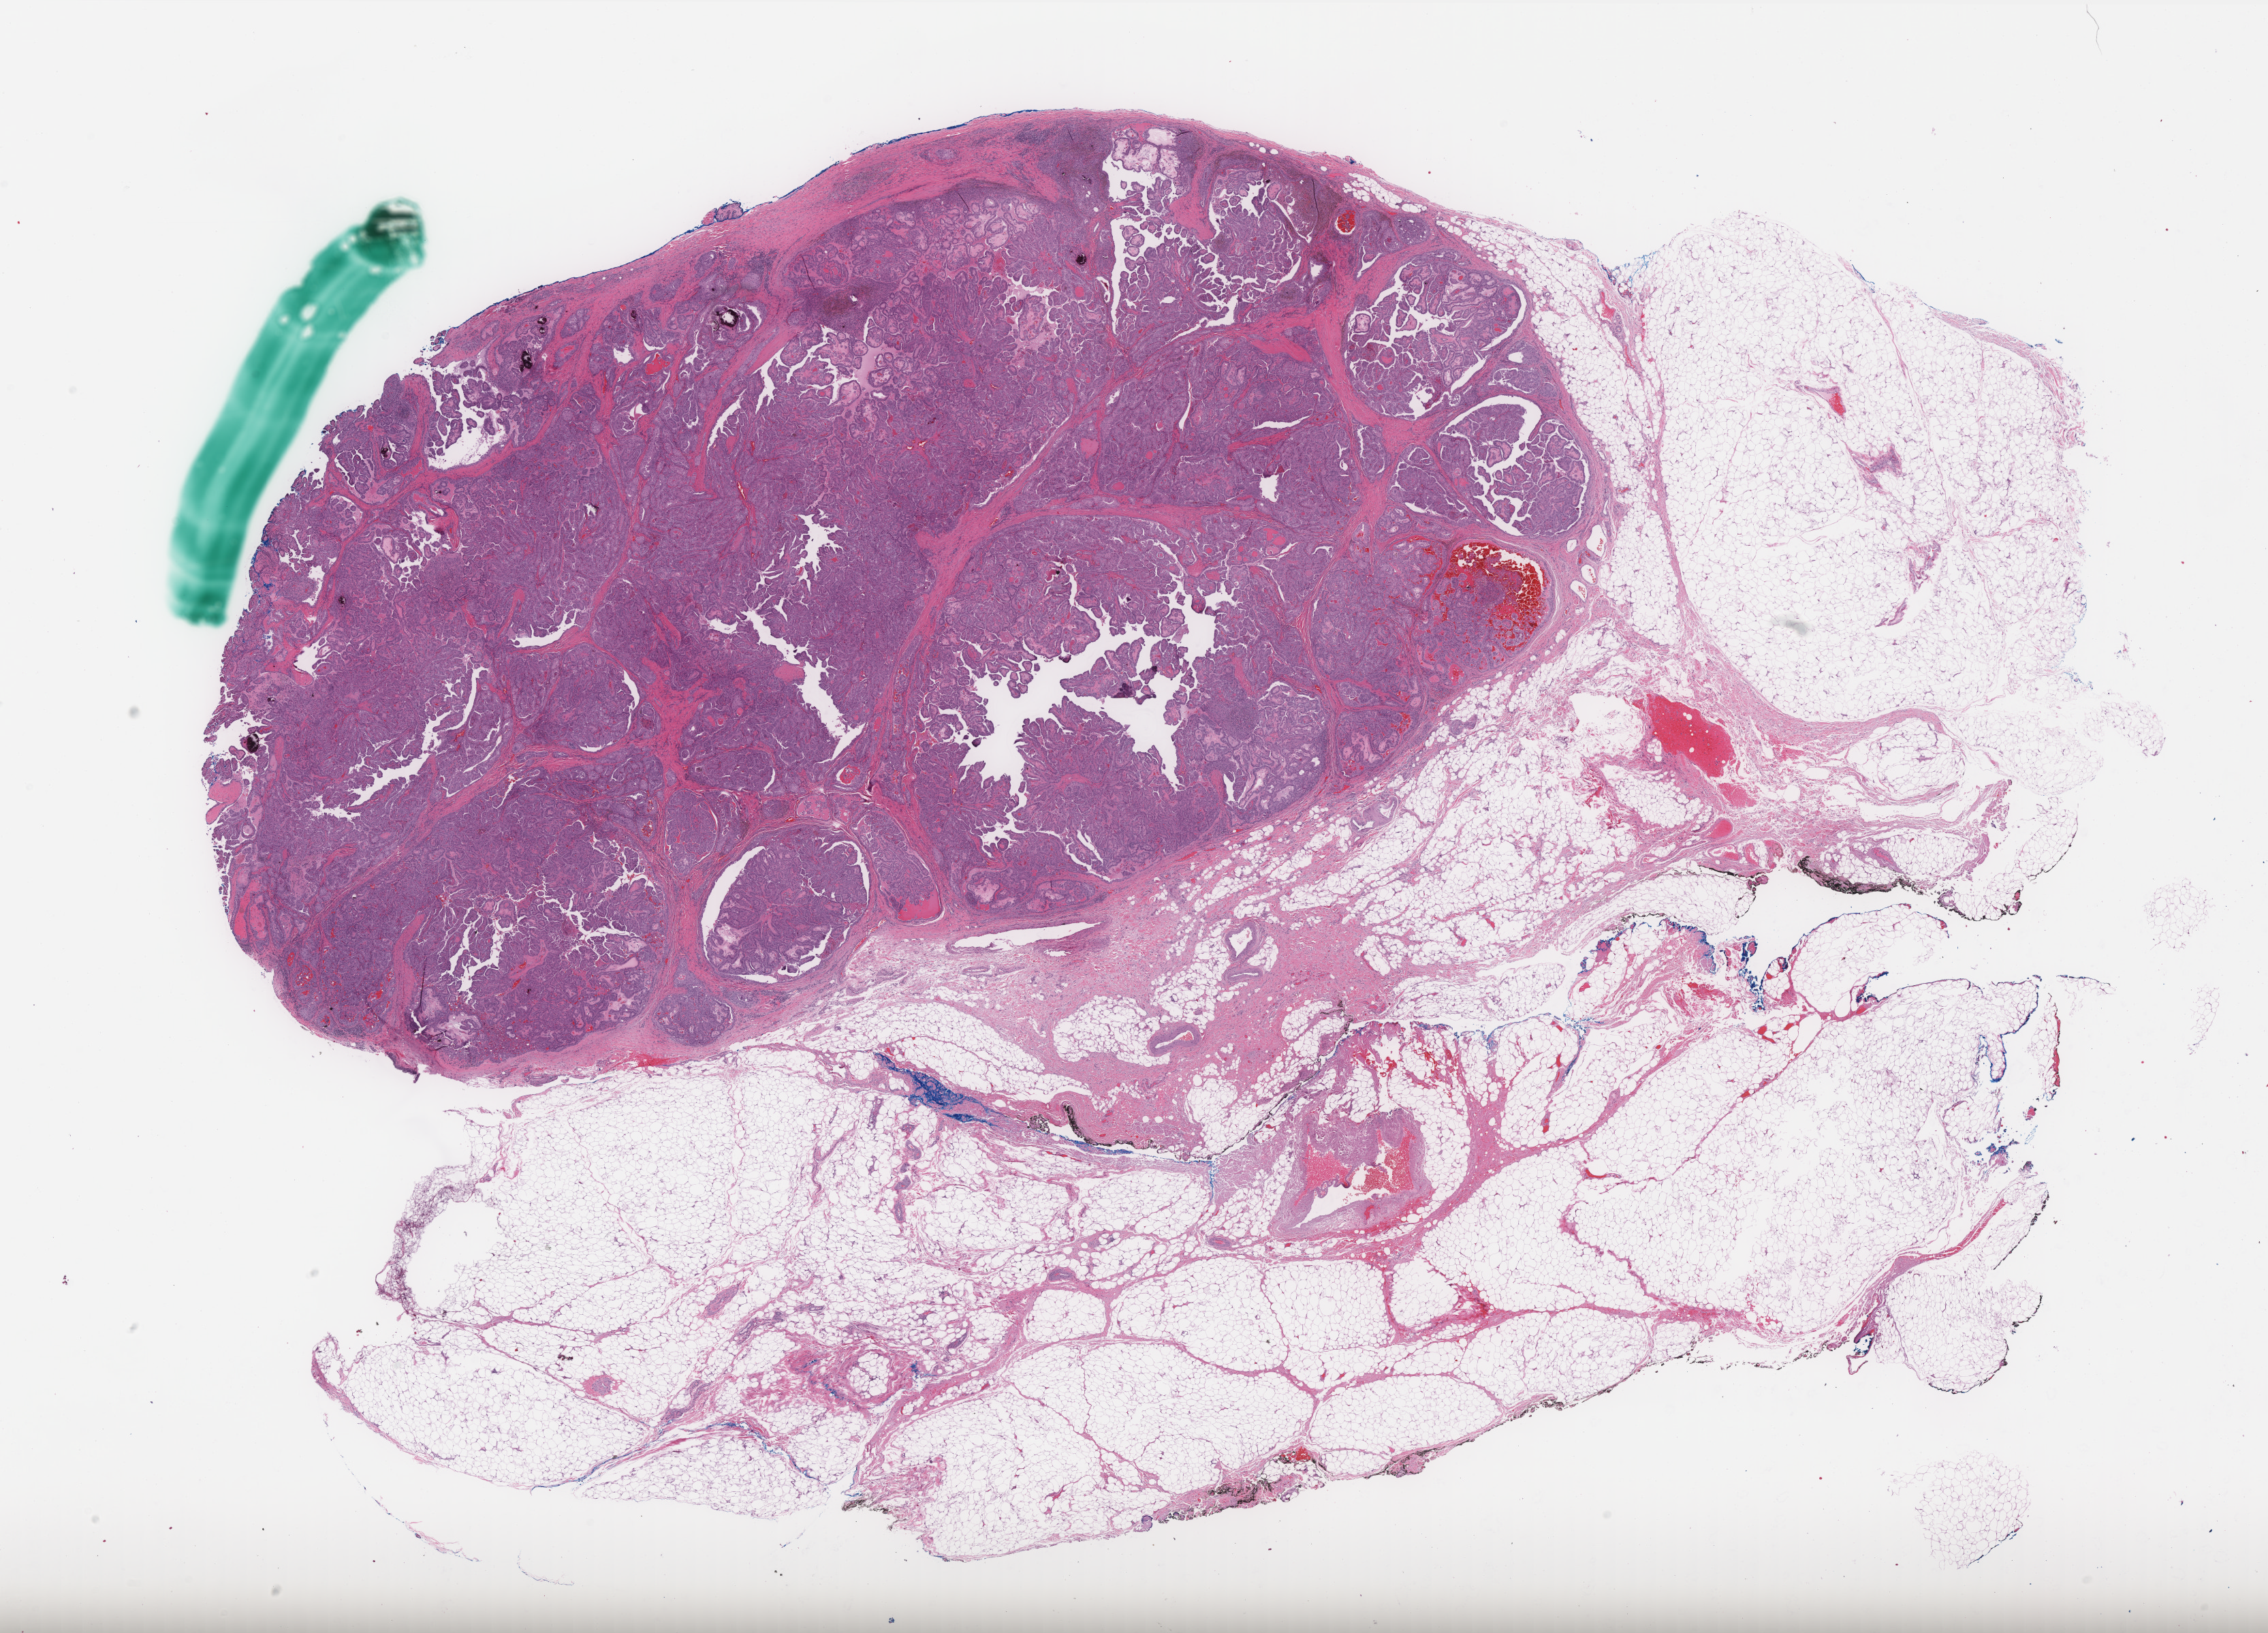
Digitized Hematoxylin and eosin (H&E) stained tissue section (whole slide), whole scanned area (about 26.7 x 19.2 mm, acquisition: 40x scan) shown as a low-resolution overview. Formalin-fixed paraffin-embedded (FFPE) diagnostic section. Primary tumour sample from the thyroid. Male patient; age at initial diagnosis 69 years.
Diagnosis: Papillary carcinoma, columnar cell (thyroid gland).